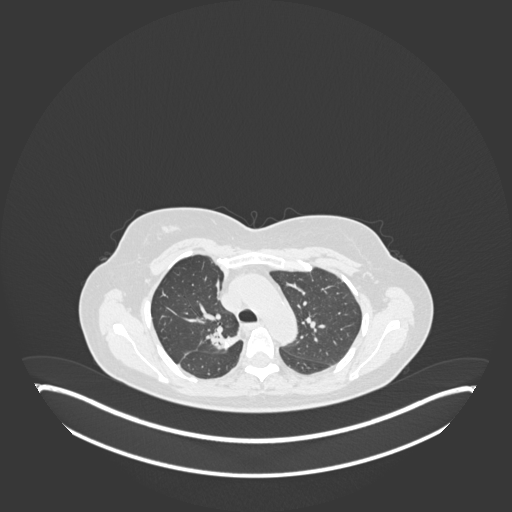
Chest CT, one axial slice. Position 125 of 181 along the scan axis. Reconstruction kernel B30f. 120 kVp. Lung window (W 1500 / L -600 HU). 512 × 512 image matrix, field of view 500 × 500 mm. Patient: female, 65 years. Case-level facts recorded for this patient, not image findings: clinical TNM (as recorded): T1b N0 M0; histopathological grade: G2.
Outlined on this slice (rectangle marked by the reading radiologist):
- lung tumour (recorded histology: adenocarcinoma): box from (x=206, y=328) to (x=240, y=353) px